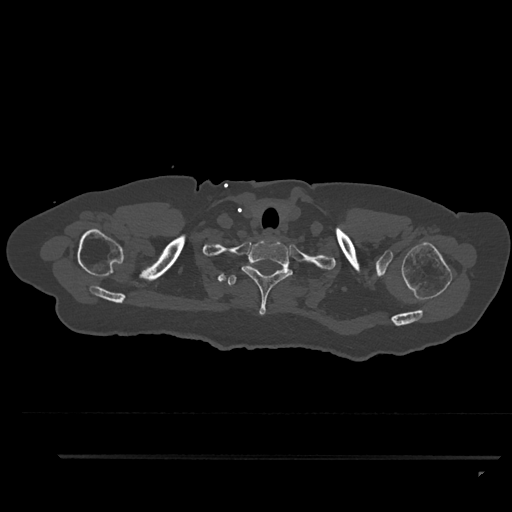
CT including the spine, one axial slice. Slice 758 of 797 in the series (ordered by position). Reconstruction kernel Br40s/3. 120 kVp. Bone window (W 1800 / L 400 HU). 512 × 512 image matrix, field of view 408 × 408 mm. Patient: female, 44 years. From the clinical record (not read from this slice): primary cancer: renal.
Outlined on this slice (semi-automatic segmentation, software-assisted and operator-edited):
- T1 vertebra: bounding box [x1, y1, x2, y2] px = [242, 240, 293, 315]
- T2 vertebra: [228, 275, 237, 286]